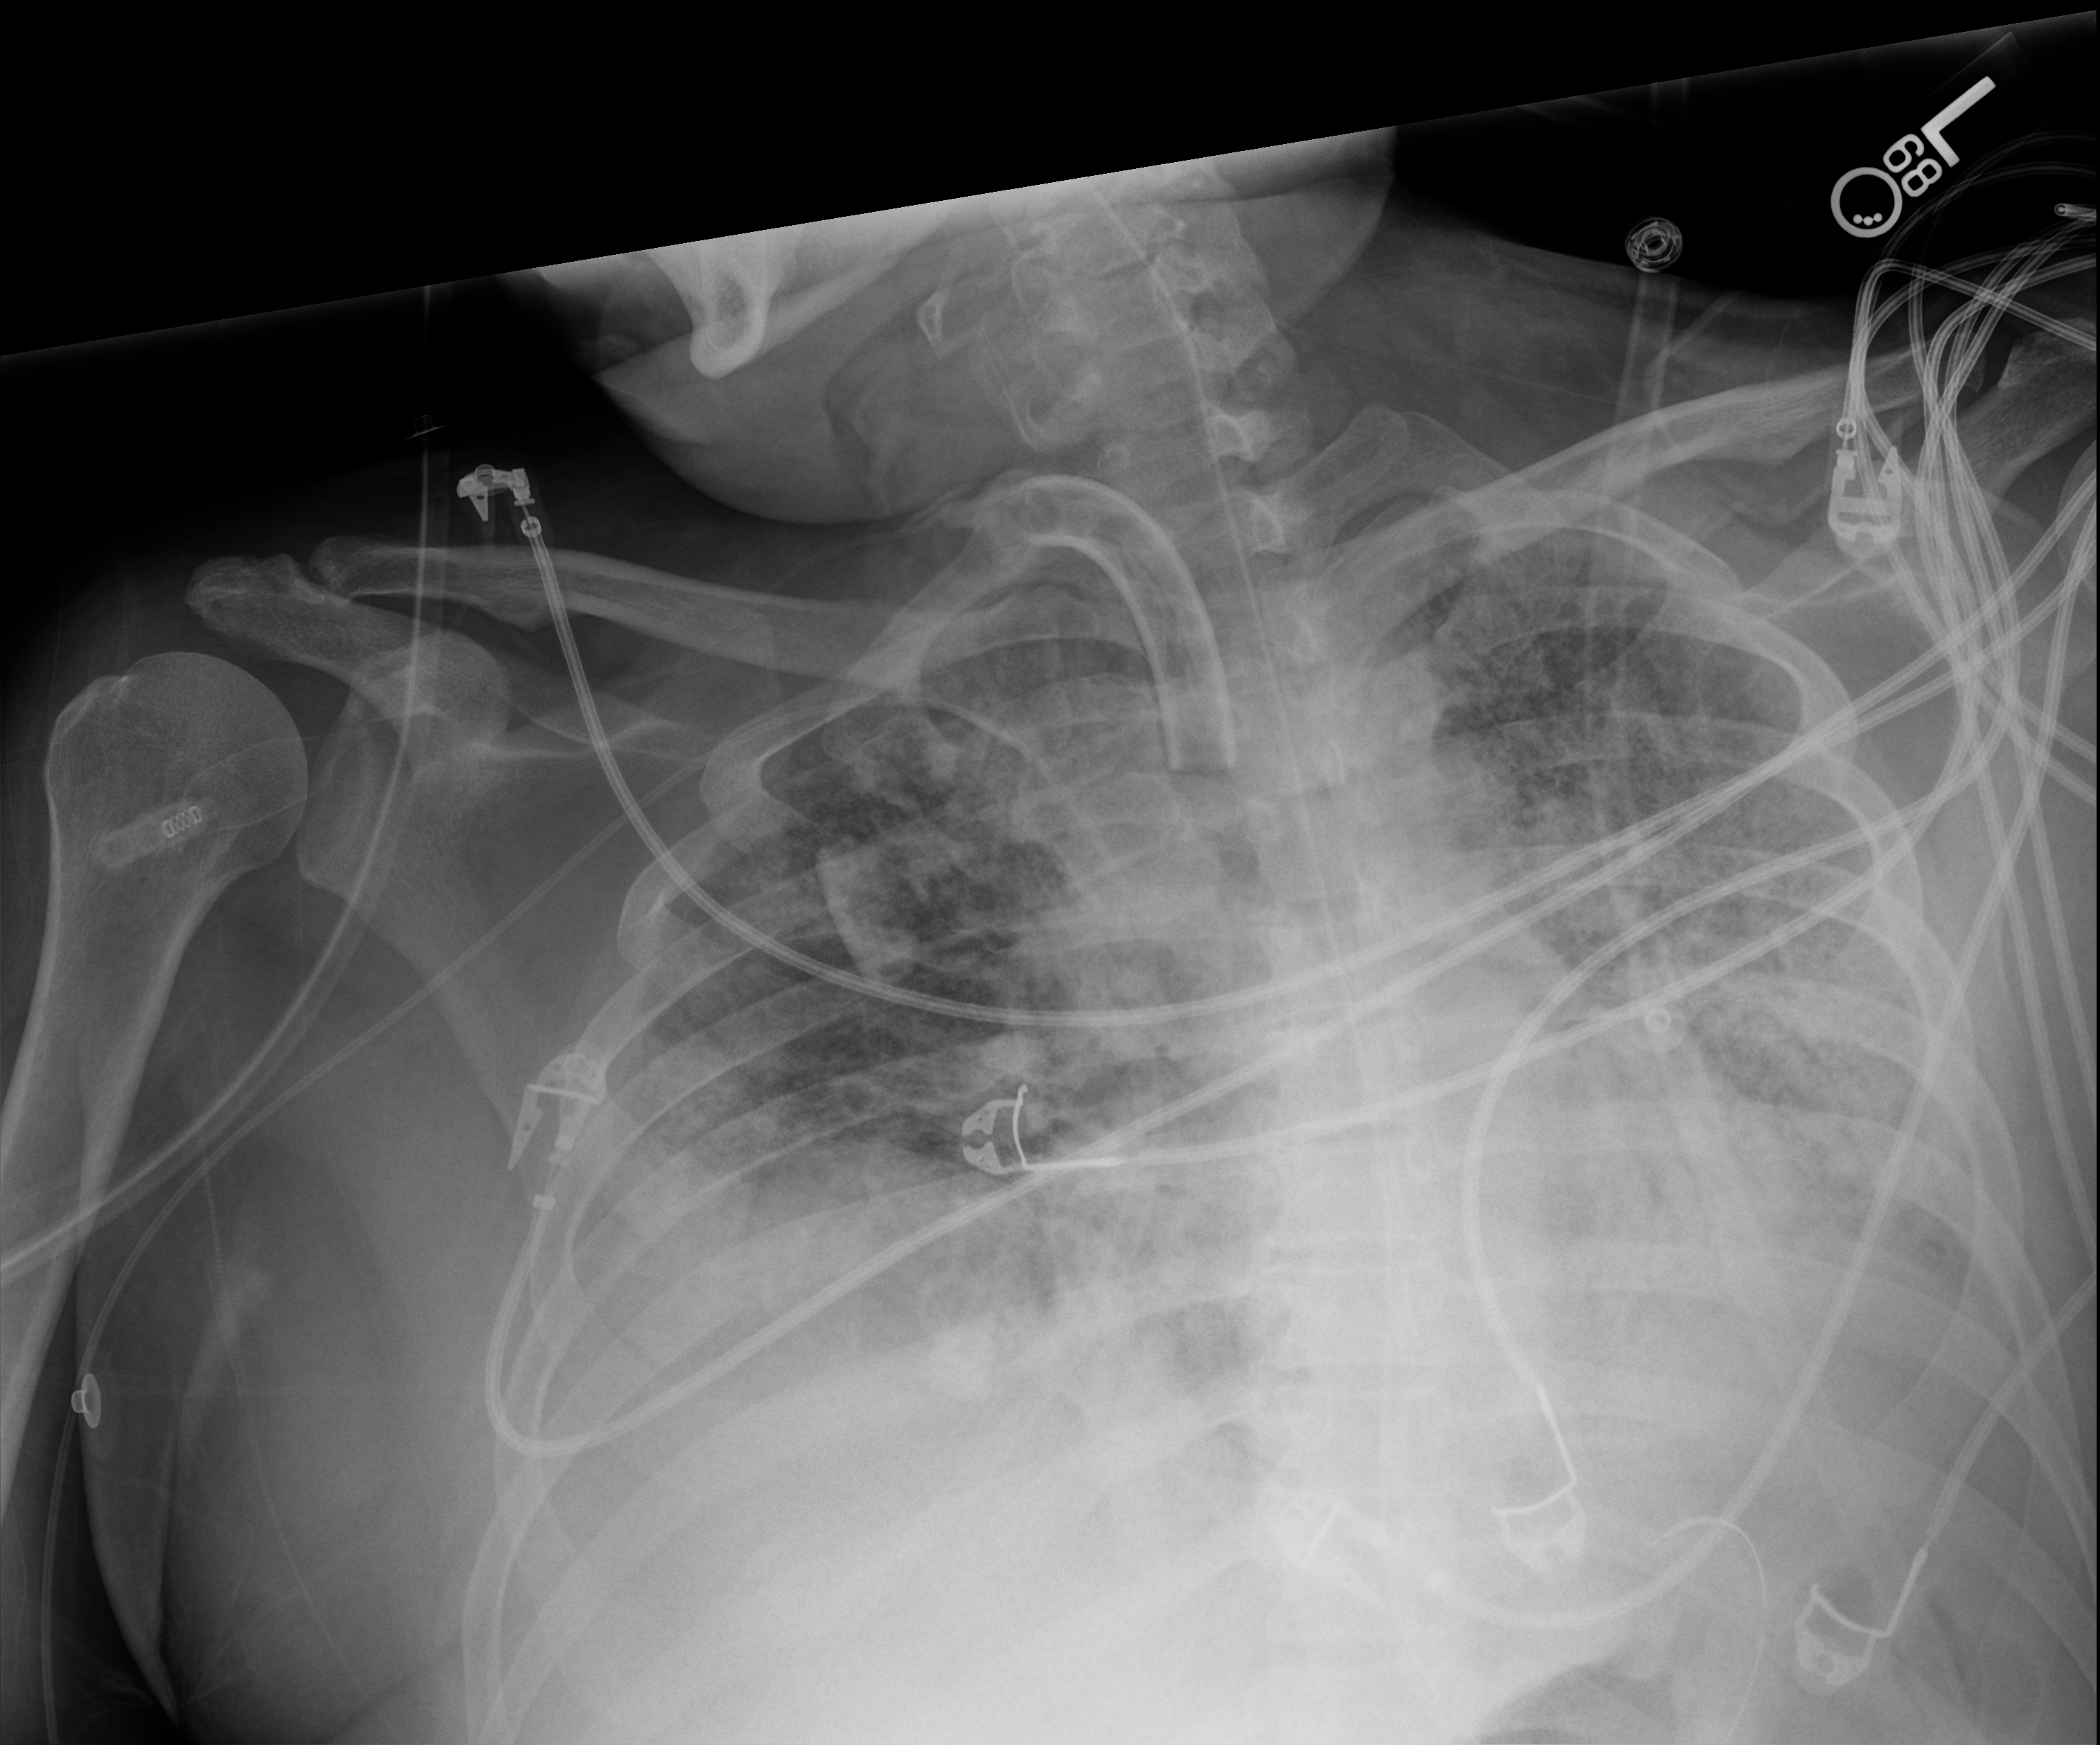
Portable chest radiograph; anteroposterior (AP) projection. Patient hospitalised with COVID-19; male, aged 18–59 years.
Hospital-stay facts (about this admission, not read from this image; timing relative to this image not recorded):
- mechanically ventilated during this hospital stay: yes
- diabetes (admission record): no